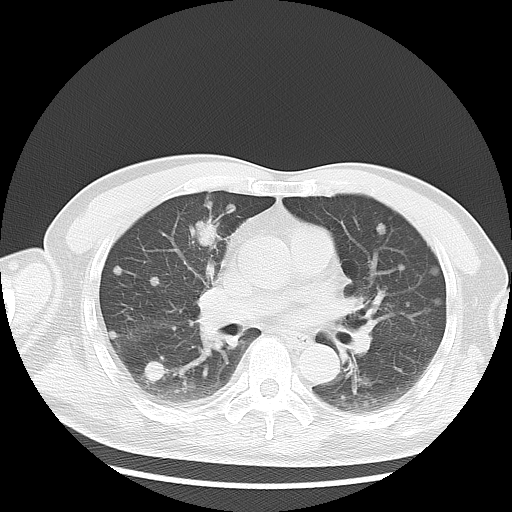
Chest CT, one axial slice; slice 11 of 35 in the series (ordered by position); reconstruction kernel LUNG; lung window (W 1500 / L -600 HU); 512 × 512 image matrix. Male patient, age 57 years. From the clinical record (not read from this slice): clinical TNM (as recorded): T2 N3 M1a.
Structures marked on this image (bounding box drawn by a radiologist):
- lung tumour (recorded histology: adenocarcinoma): box from (x=194, y=218) to (x=220, y=251) px